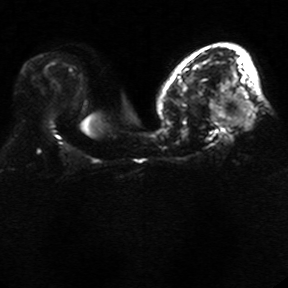
Breast MRI, one axial slice; position 16 of 34 along the scan axis; diffusion-weighted series; image 2 of 4 stored at this slice position (different b-values; order by instance number); 1.5 T; 5 mm slice thickness; 288 × 288 image matrix. Female patient.
Annotated regions visible in this slice (manually delineated by an expert):
- tumour on diffusion-weighted imaging: bounding box <208,87,250,130> (left, top, right, bottom; pixels)